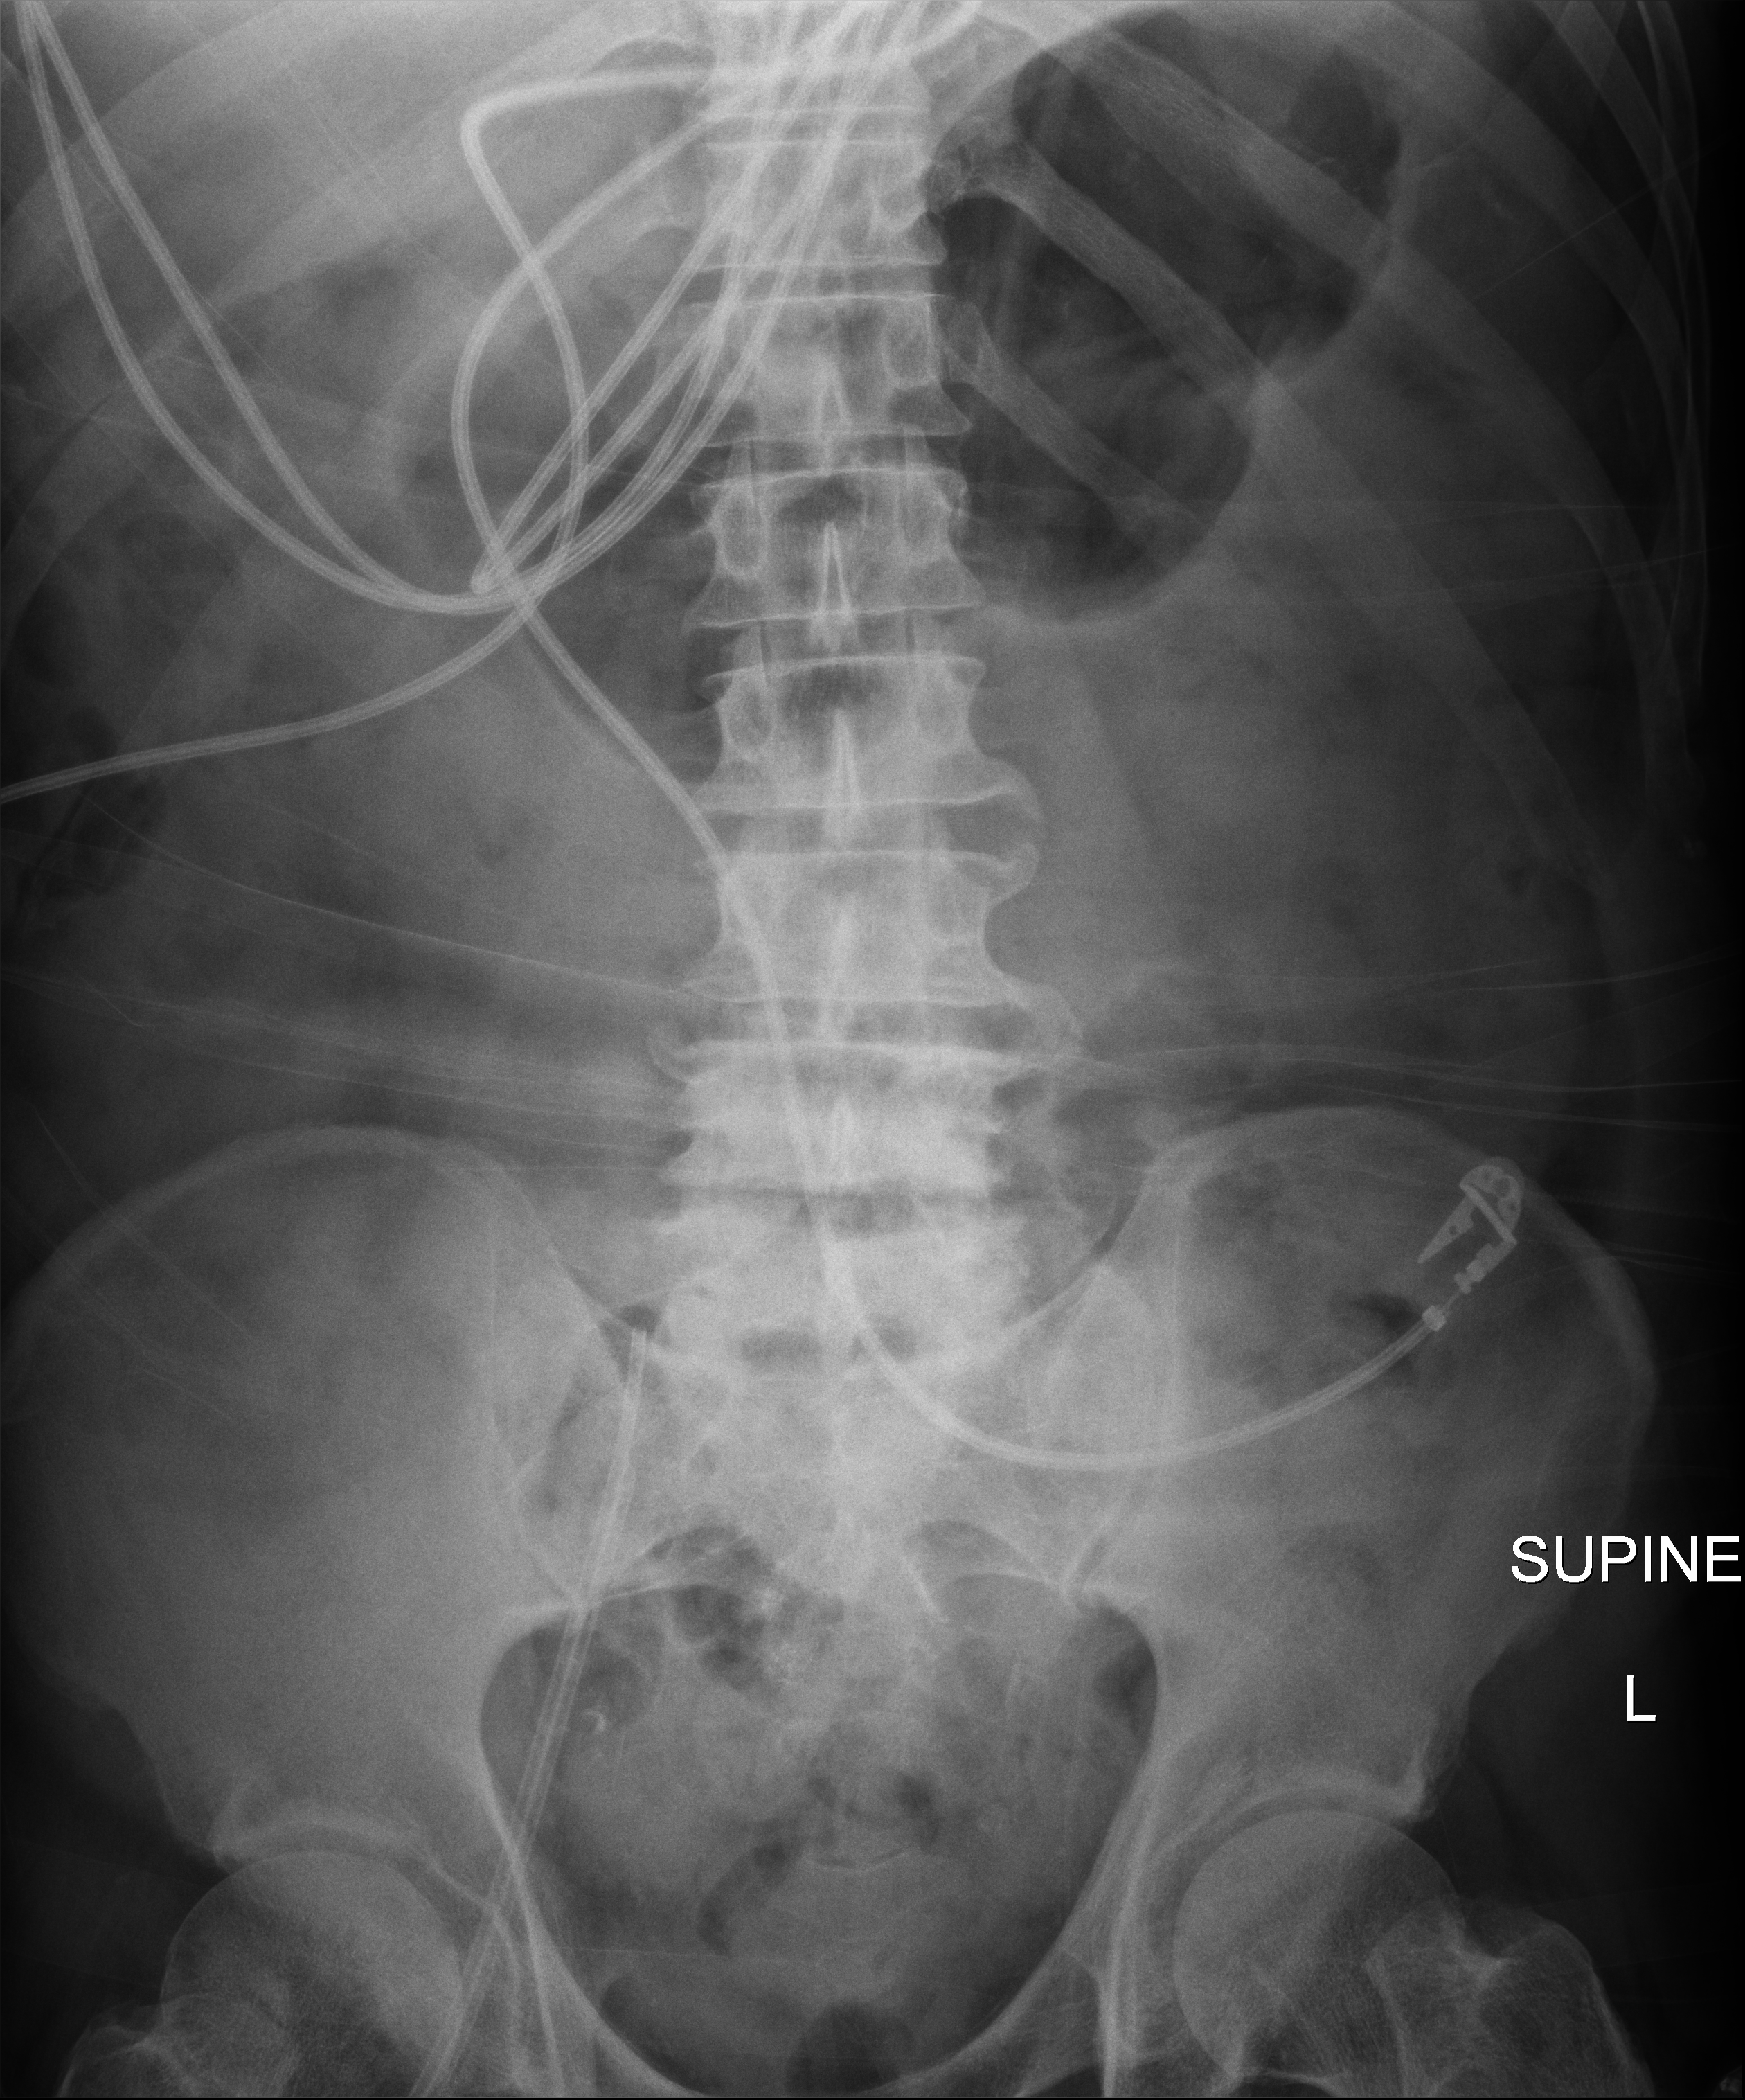
Abdomen X-ray (portable), anteroposterior (AP) projection. Male patient hospitalised with COVID-19, age 60–74 years.
From the hospital-stay record, not from the radiograph (when in the stay this image was taken is not recorded): mechanically ventilated during this hospital stay: yes.